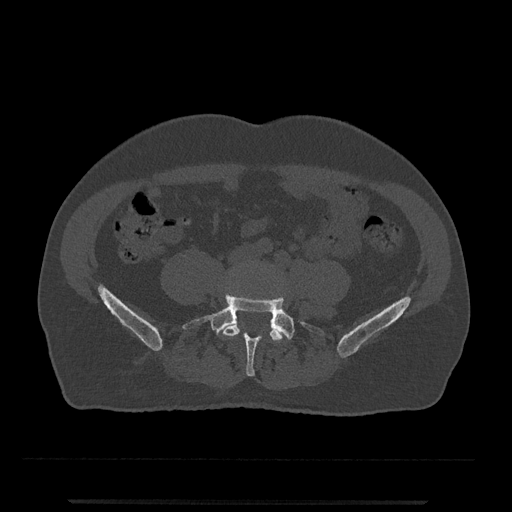
CT including the spine, one axial slice. Slice 91 of 797 in the series (ordered by position). Reconstruction kernel Br40s/3. 120 kVp. Bone window (W 1800 / L 400 HU). 512 × 512 image matrix. Patient: male, 63 years. From the clinical record (not read from this slice): primary cancer: prostate.
Structures marked on this image (semi-automatically segmented with operator editing):
- L4 vertebra: bounding box [x1, y1, x2, y2] px = [222, 319, 283, 345]
- L5 vertebra: [183, 295, 323, 377]